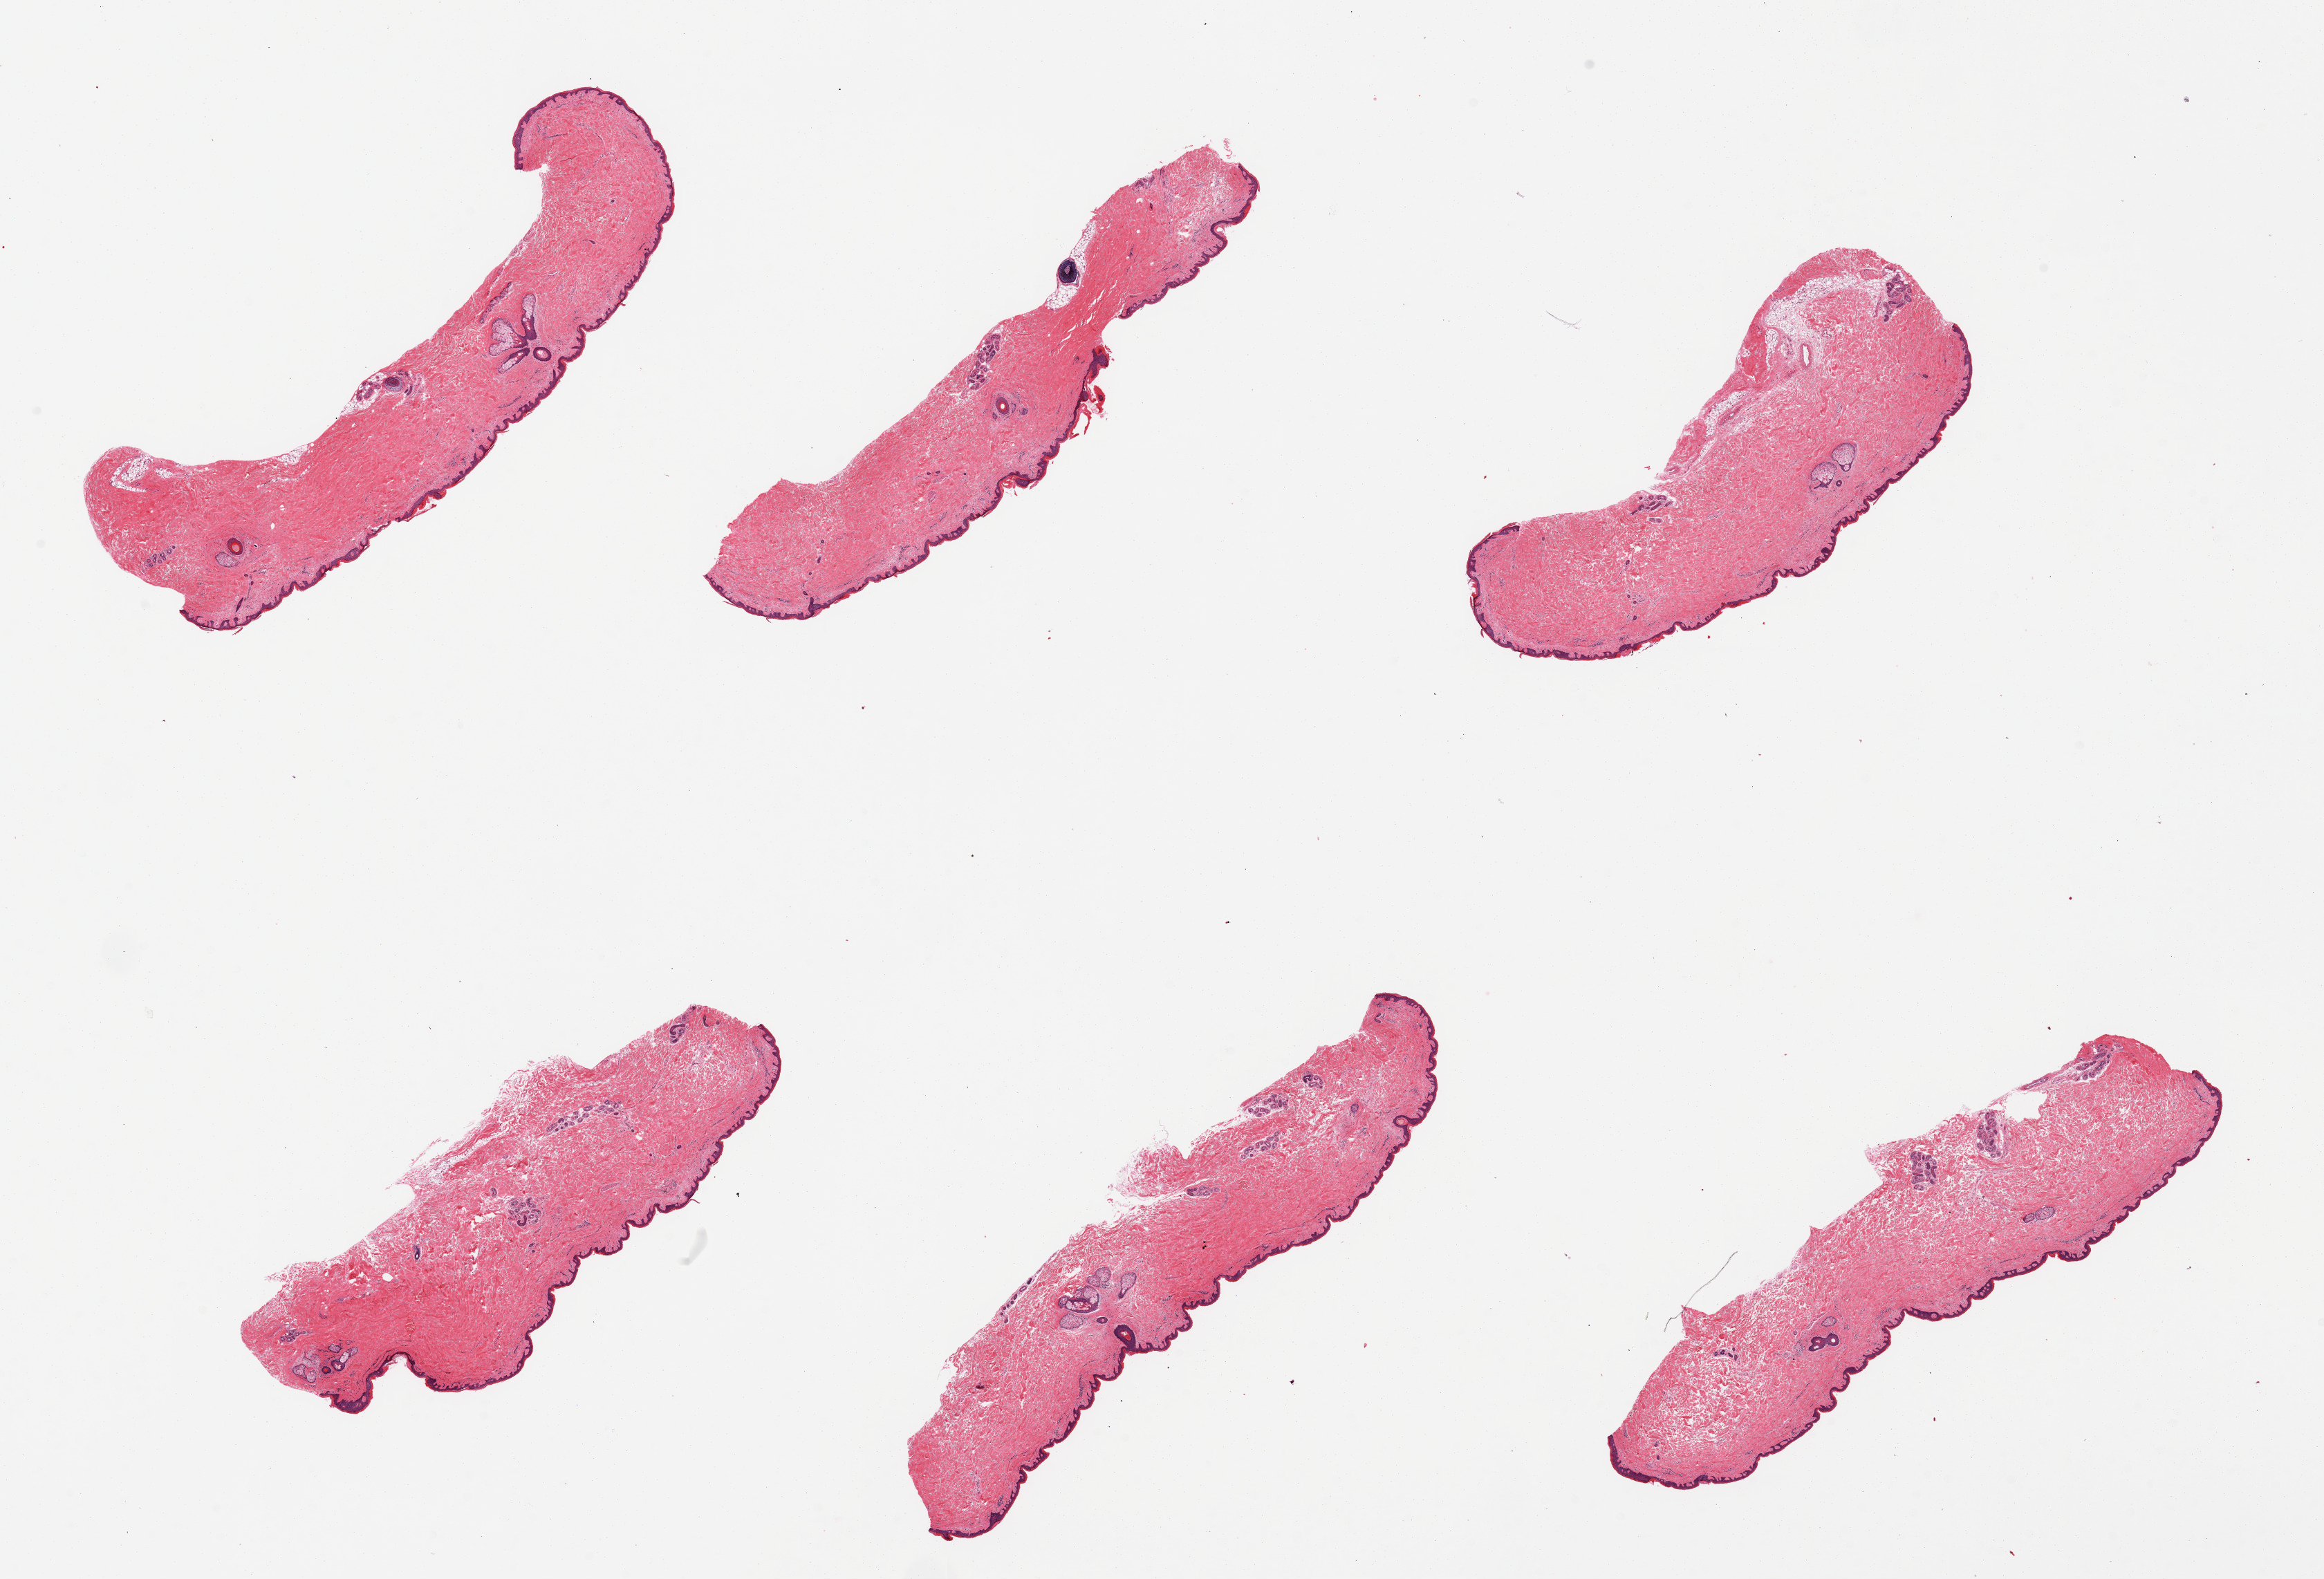
H&E whole-slide image, low-resolution overview of the scanned area, about 26.6 x 18.1 mm (slide scanned at 20x). PAXgene-fixed paraffin-embedded (PFPE) section. Target tissue: skin of suprapubic region. Tissue donor sample.
* review note (as recorded): 6 pieces, minimal dermal fat; squamous epithelium is ~50 microns